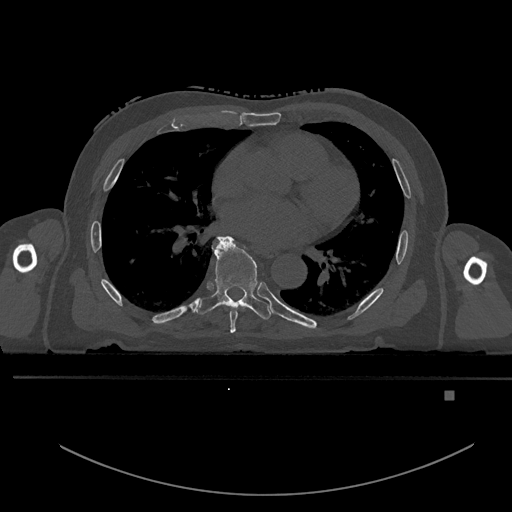
CT including the spine, one axial slice. Slice 269 of 969 in the series (ordered by position). Bone window (W 1800 / L 400 HU). 0.5 mm slice thickness. 512 × 512 image matrix, field of view 456 × 456 mm. Patient: male, 82 years. From the clinical record (not read from this slice): primary cancer: prostate.
Annotated regions visible in this slice (semi-automatically segmented with operator editing):
- T6 vertebra: bounding box (x1, y1, x2, y2) in pixels: (229, 306, 239, 333)
- T7 vertebra: (194, 235, 271, 320)